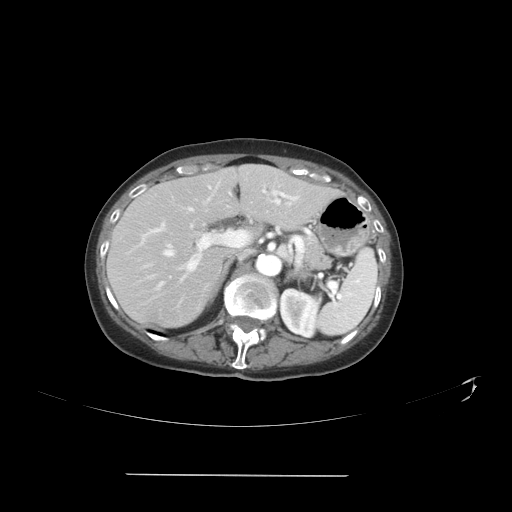
Contrast-enhanced abdominal CT, one axial slice; slice 24 of 41 in the series (ordered by position); reconstruction kernel STANDARD; soft-tissue window (W 400 / L 40 HU); 5 mm slice thickness; 512 × 512 image matrix. Female patient, age 74 years. Case-level facts recorded for this patient, not image findings: diagnosis: colorectal cancer liver metastases, imaged before liver resection; multiple liver metastases: yes; largest metastasis: 3.3 cm; disease in both lobes: yes.
Outlined on this slice (outlined manually by an expert reader):
- hepatic veins: bounding box <157,192,280,289> (left, top, right, bottom; pixels)
- liver: <109,165,337,327>
- planned liver remnant (the part of the liver to remain after resection): <117,165,313,245>
- portal vein (with intrahepatic branches): <142,190,296,271>